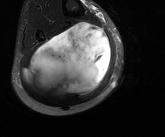
MRI of an extremity soft-tissue mass, one axial slice; slice 68 of 81 in the series (ordered by position); T2-weighted fat-saturated; MR volume resampled by the dataset authors to the PET/CT grid (not the native acquisition matrix); 3.27 mm slice thickness; 165 × 137 image matrix. Male patient. Case-level facts recorded for this patient, not image findings: histological type: liposarcoma - round cell; grade: high; site of the primary tumour: right calf.
Outlined on this slice (expert contour drawn on MRI and transferred to this co-registered scan by the dataset authors):
- gross tumour volume (mass): box from (x=23, y=23) to (x=111, y=95) px